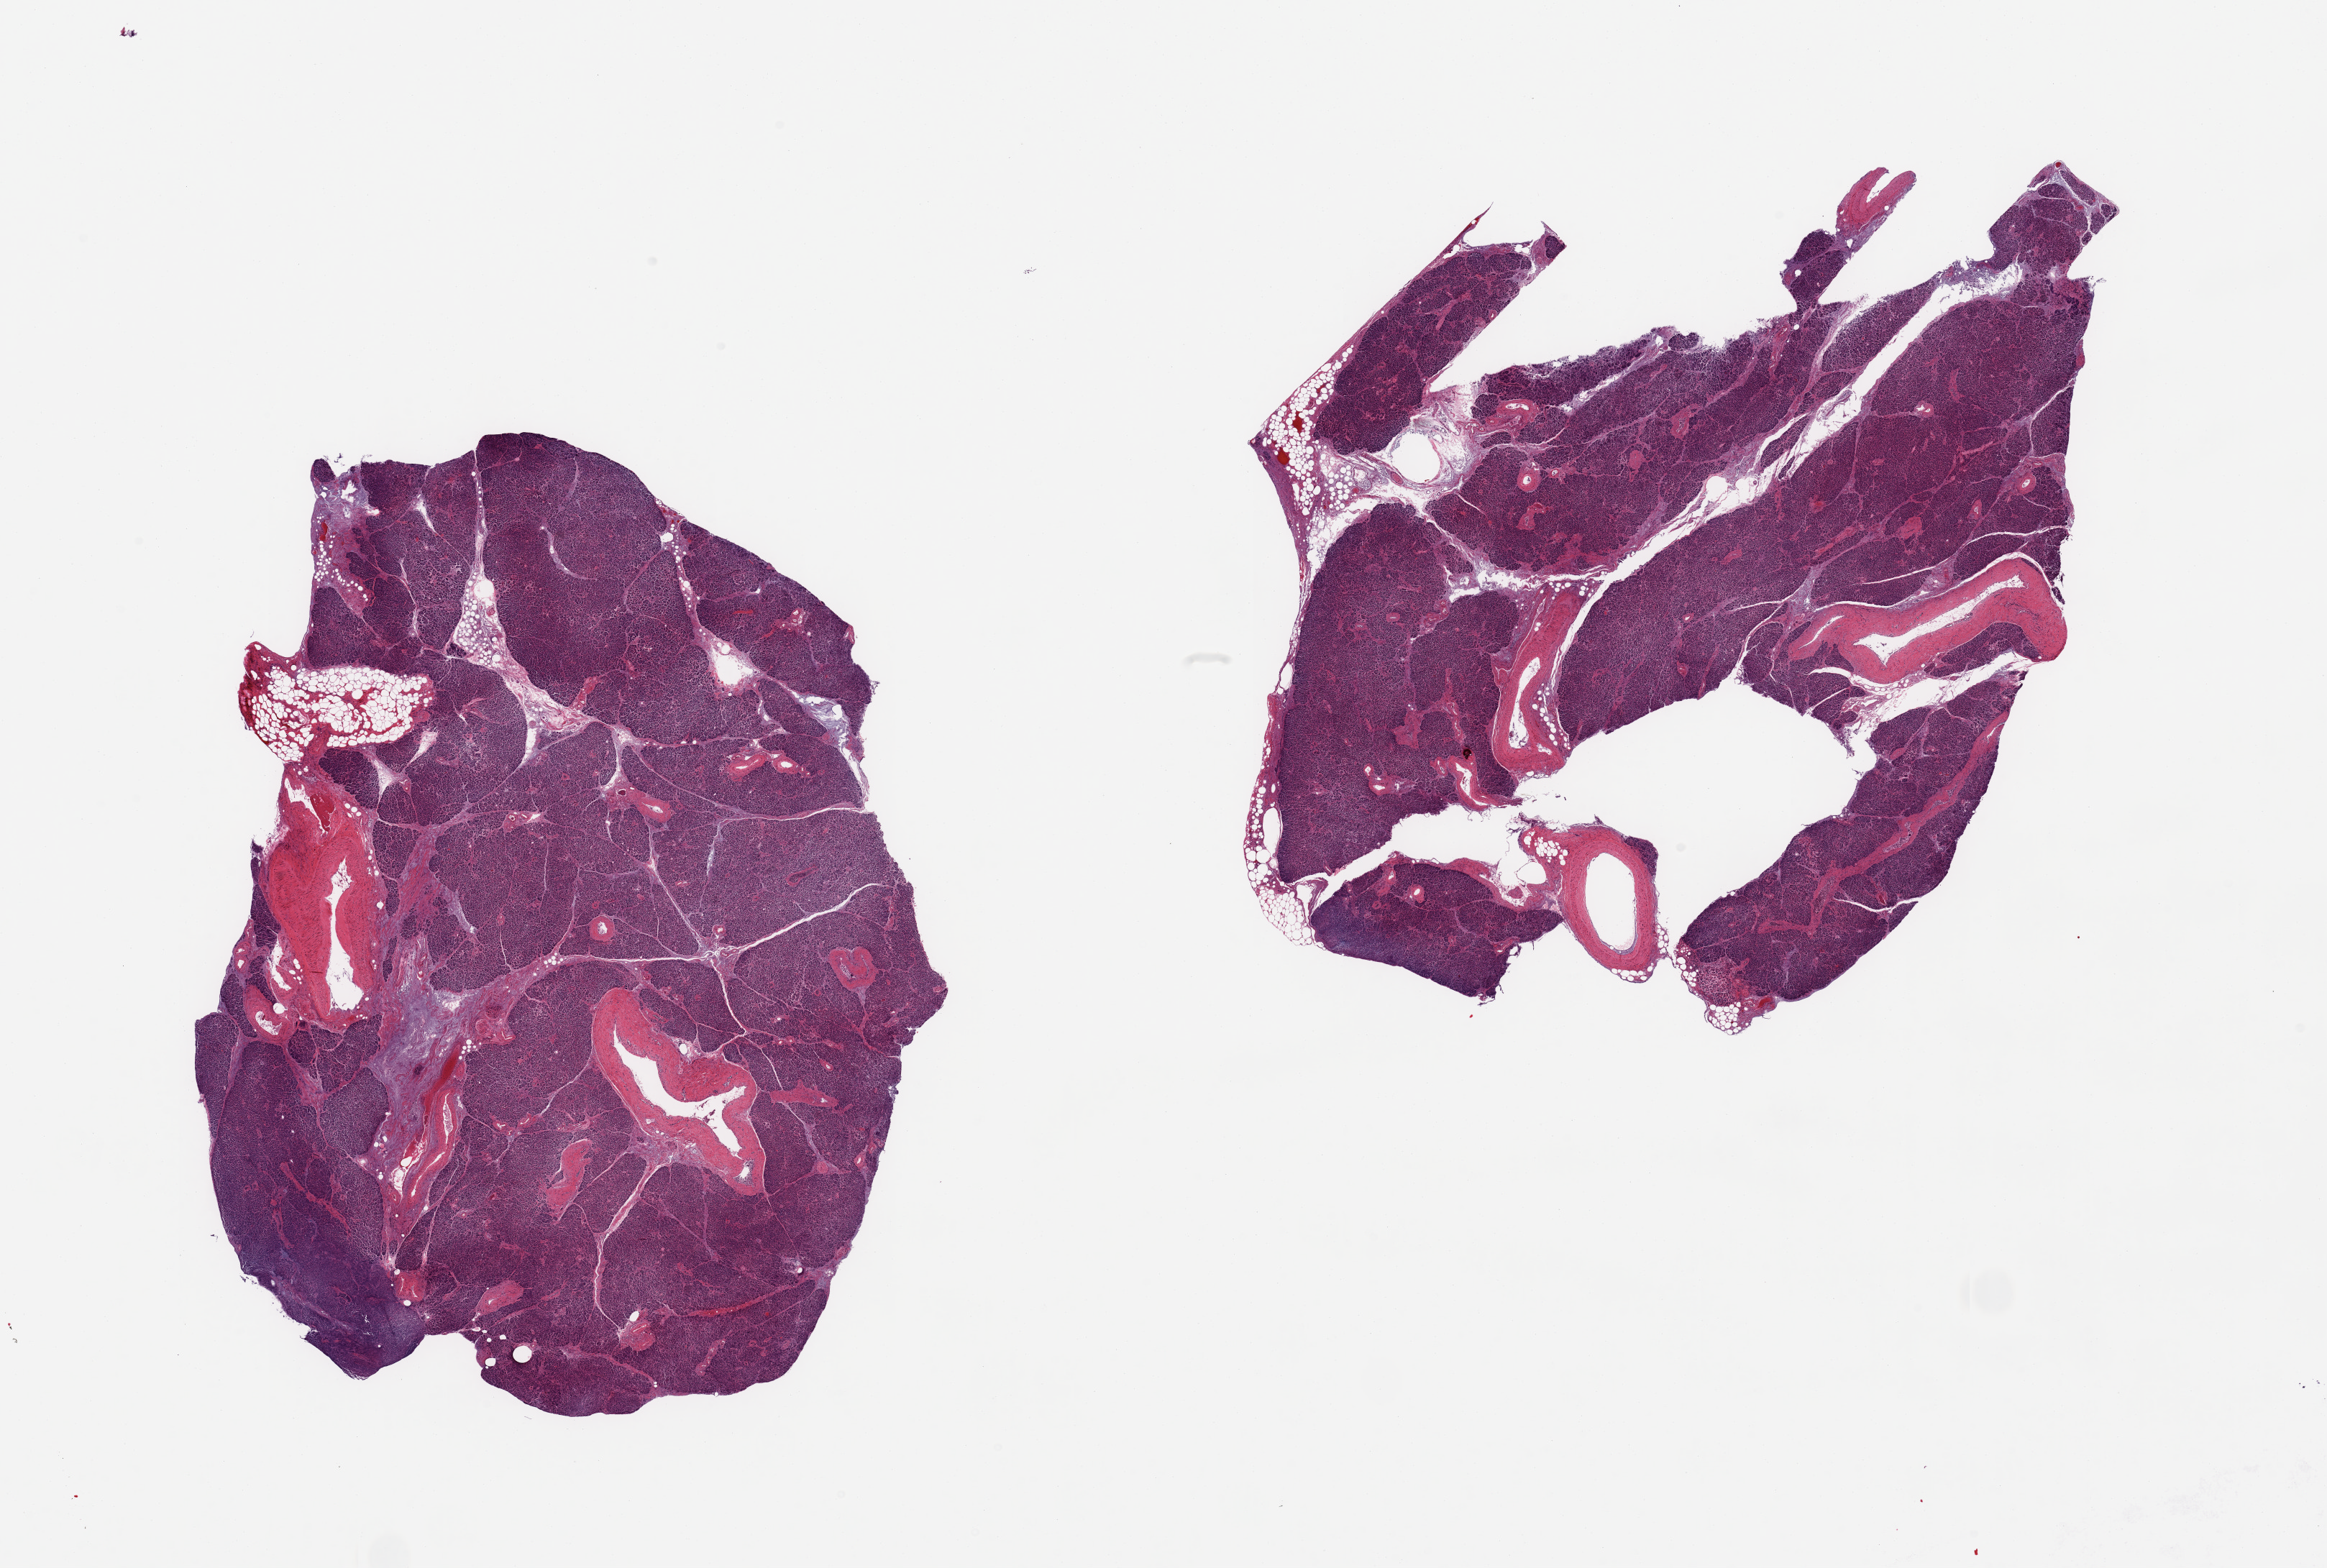
Whole-slide image, H&E stain, a low-resolution overview of the entire scanned area, about 25.6 x 17.3 mm; PAXgene-fixed, paraffin-embedded tissue; target tissue: pancreas; donor tissue sample. Male donor.
- reviewer comment on this tissue sample: 2 pieces; ~5% internal fat; moderate to severe autolysis